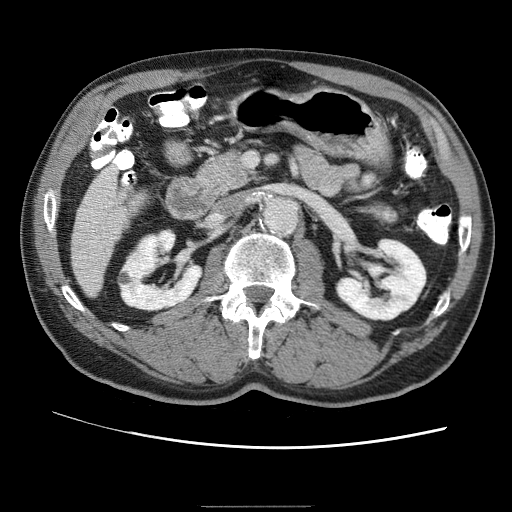
Contrast-enhanced abdominal CT (liver protocol), one axial slice. Slice 11 of 75 in the series (ordered by position). 120 kVp. One of 2 acquisitions stored at this slice position. Soft-tissue window (W 400 / L 40 HU). 512 × 512 image matrix. Case-level facts recorded for this patient, not image findings: diagnosis: hepatocellular carcinoma (patient treated with transarterial chemoembolisation; whether this scan precedes or follows treatment is not stated here); TNM stage (as recorded): Stage-II; Child-Pugh class: A; tumour differentiation: well differentiated; tumour size: 2 cm.
Annotated regions visible in this slice (semi-automatic segmentation, software-assisted and operator-edited):
- liver parenchyma outside the tumour (the mass and vessels are separate outlines, so this box may not span the whole liver): bounding box [x1, y1, x2, y2] px = [72, 168, 120, 287]
- liver vessels: [79, 172, 116, 250]